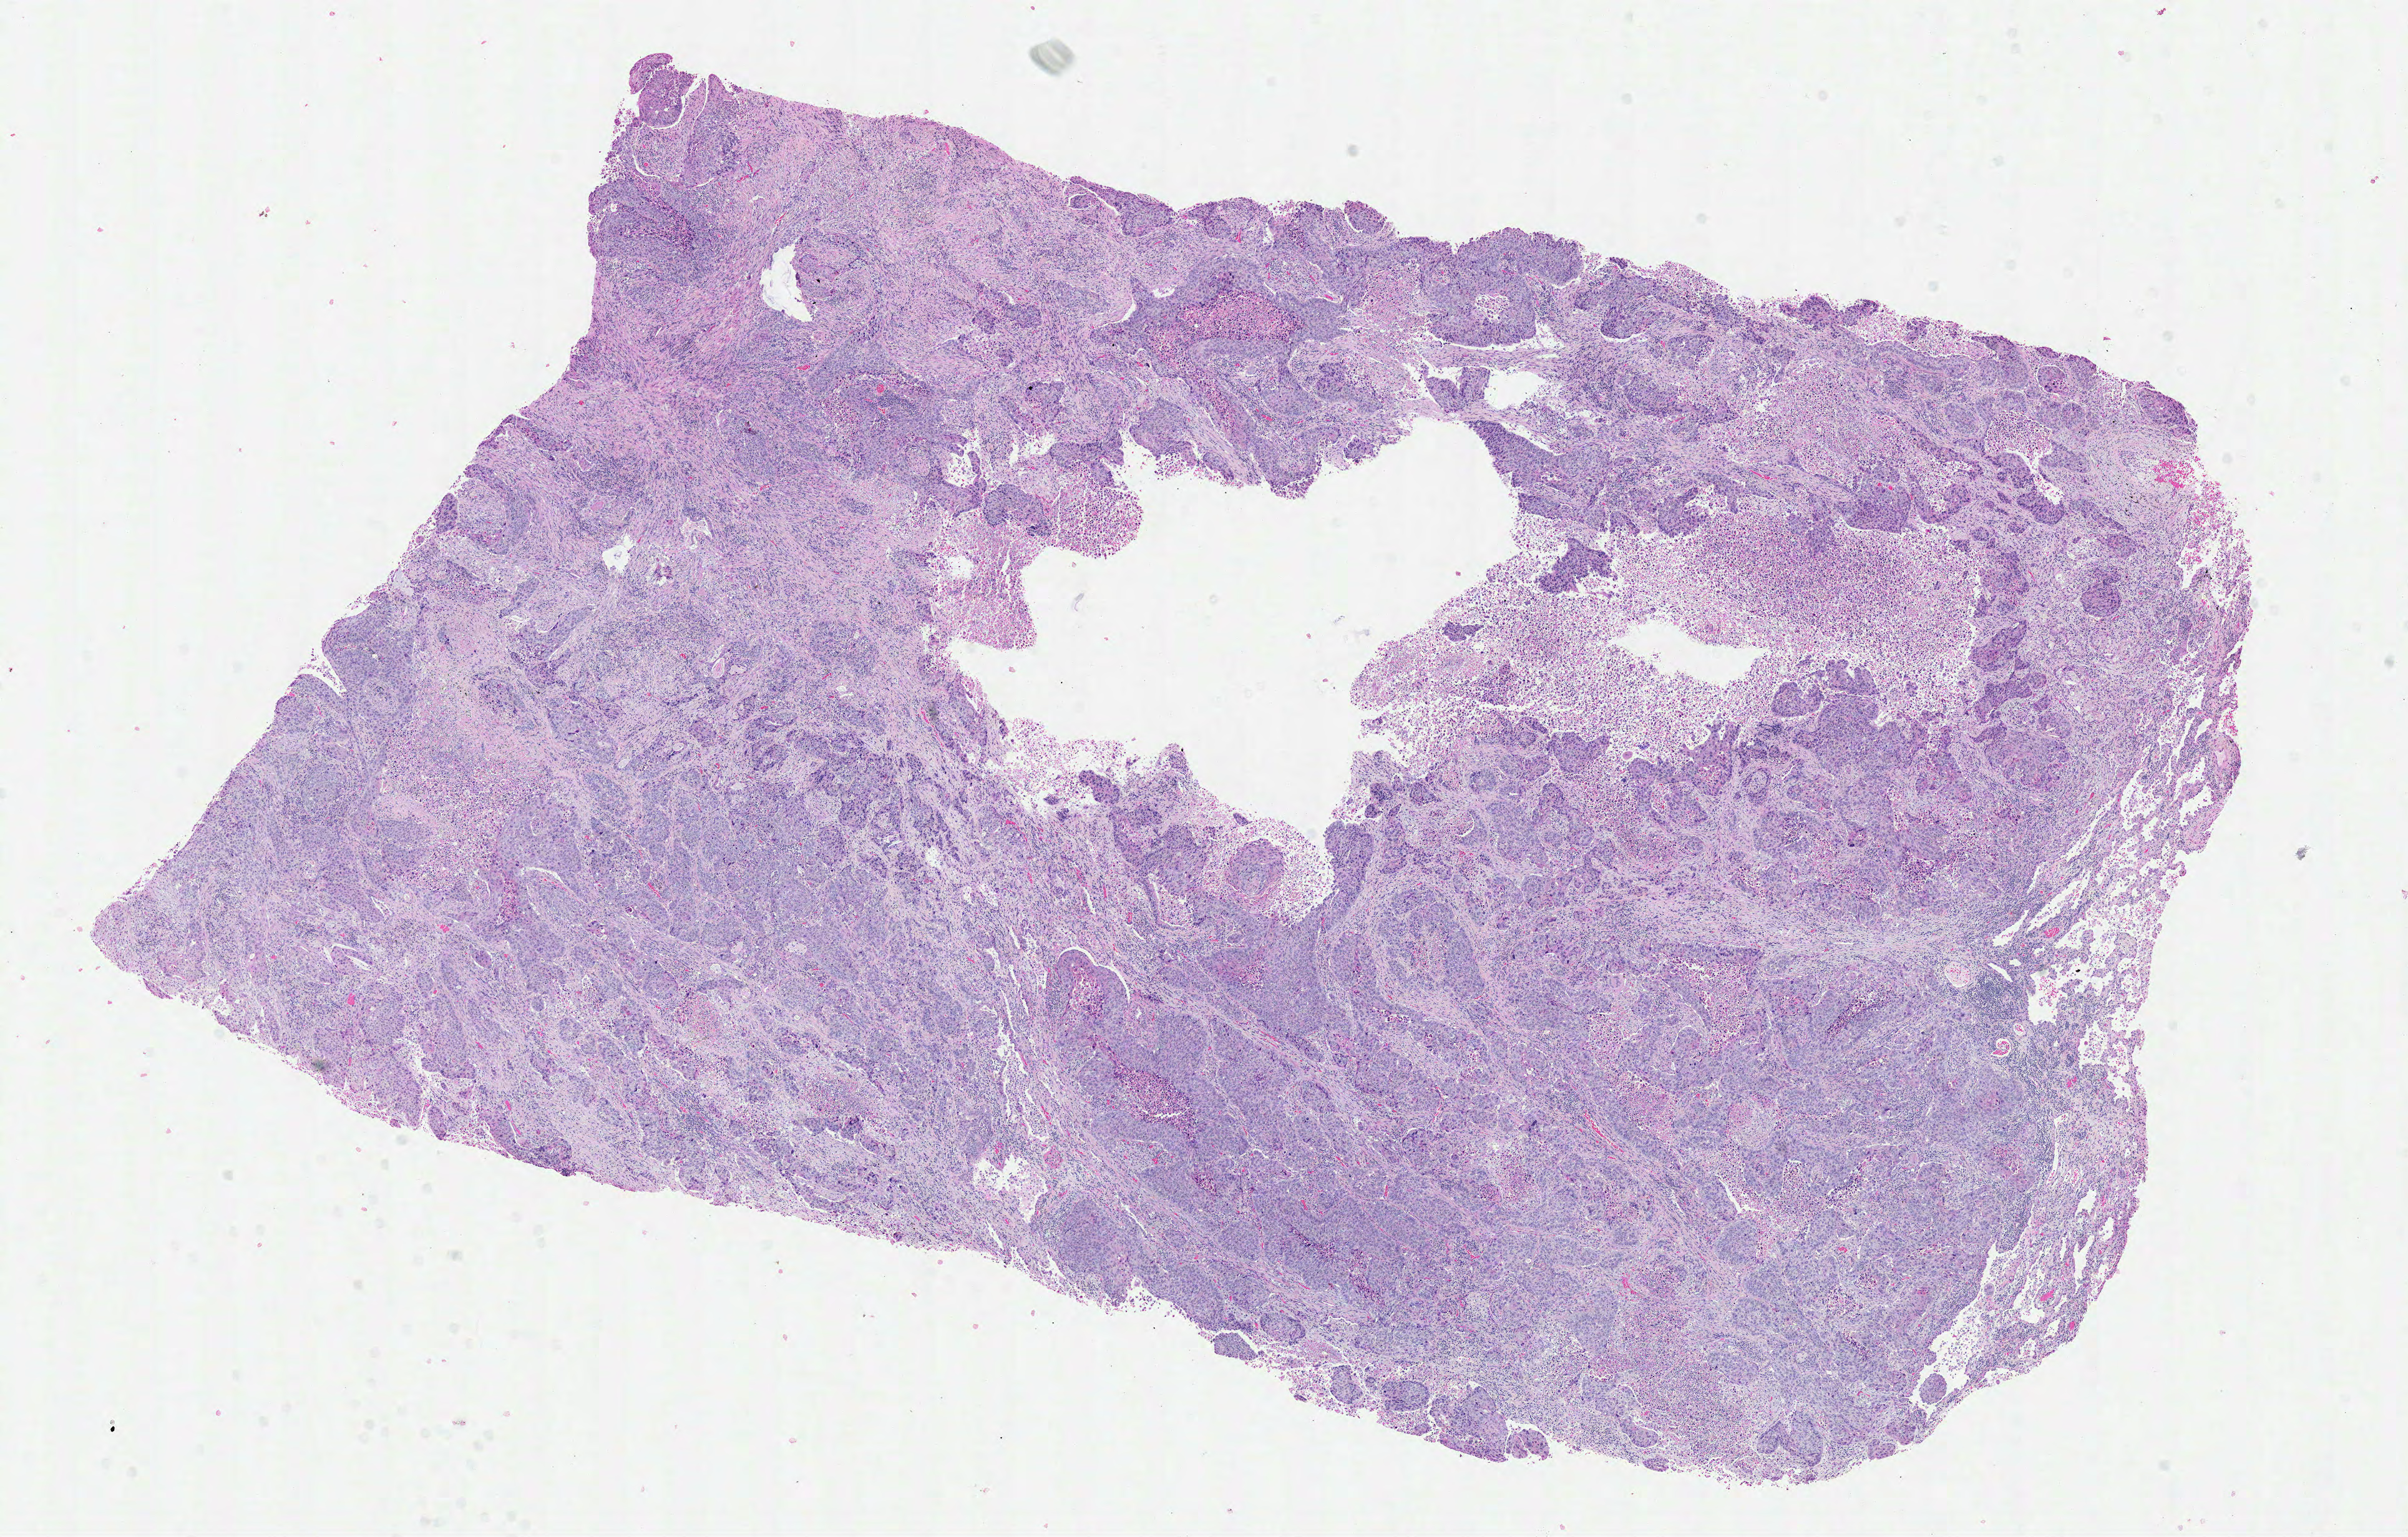
Digitized H&E tissue section (whole slide), whole scanned area (about 15.2 x 9.7 mm, slide scanned at 40x) shown as a low-resolution overview; formalin-fixed paraffin-embedded (FFPE) diagnostic section; lung, primary tumour sample. Patient: male, age at initial diagnosis 68 years.
AJCC pathologic stage: IIIB (6th edition). Diagnosis: Squamous cell carcinoma, NOS (upper lobe, lung). Laterality: left.